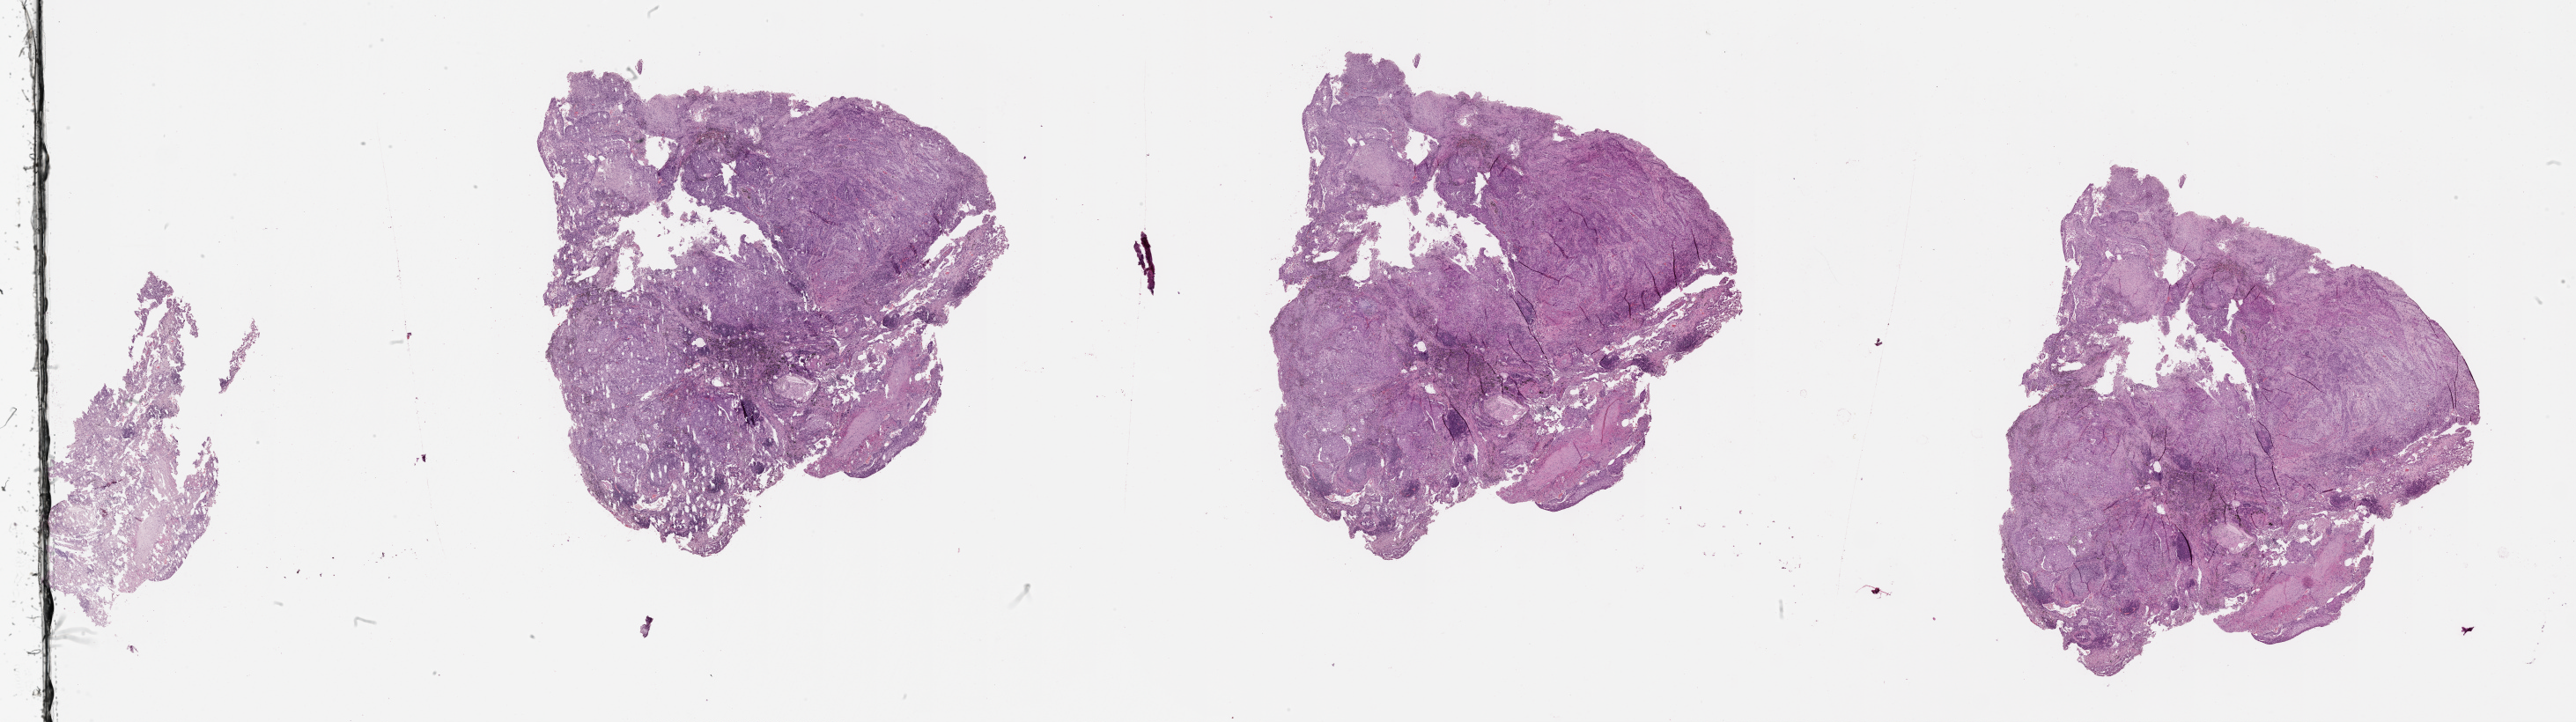
H&E-stained whole-slide image — whole scanned area (about 47.1 x 13.2 mm) shown as a low-resolution overview. Tumour tissue sample, lung. Patient: male, age 68 years.
* patient diagnosis (cohort enrolment): squamous cell carcinoma (lung)